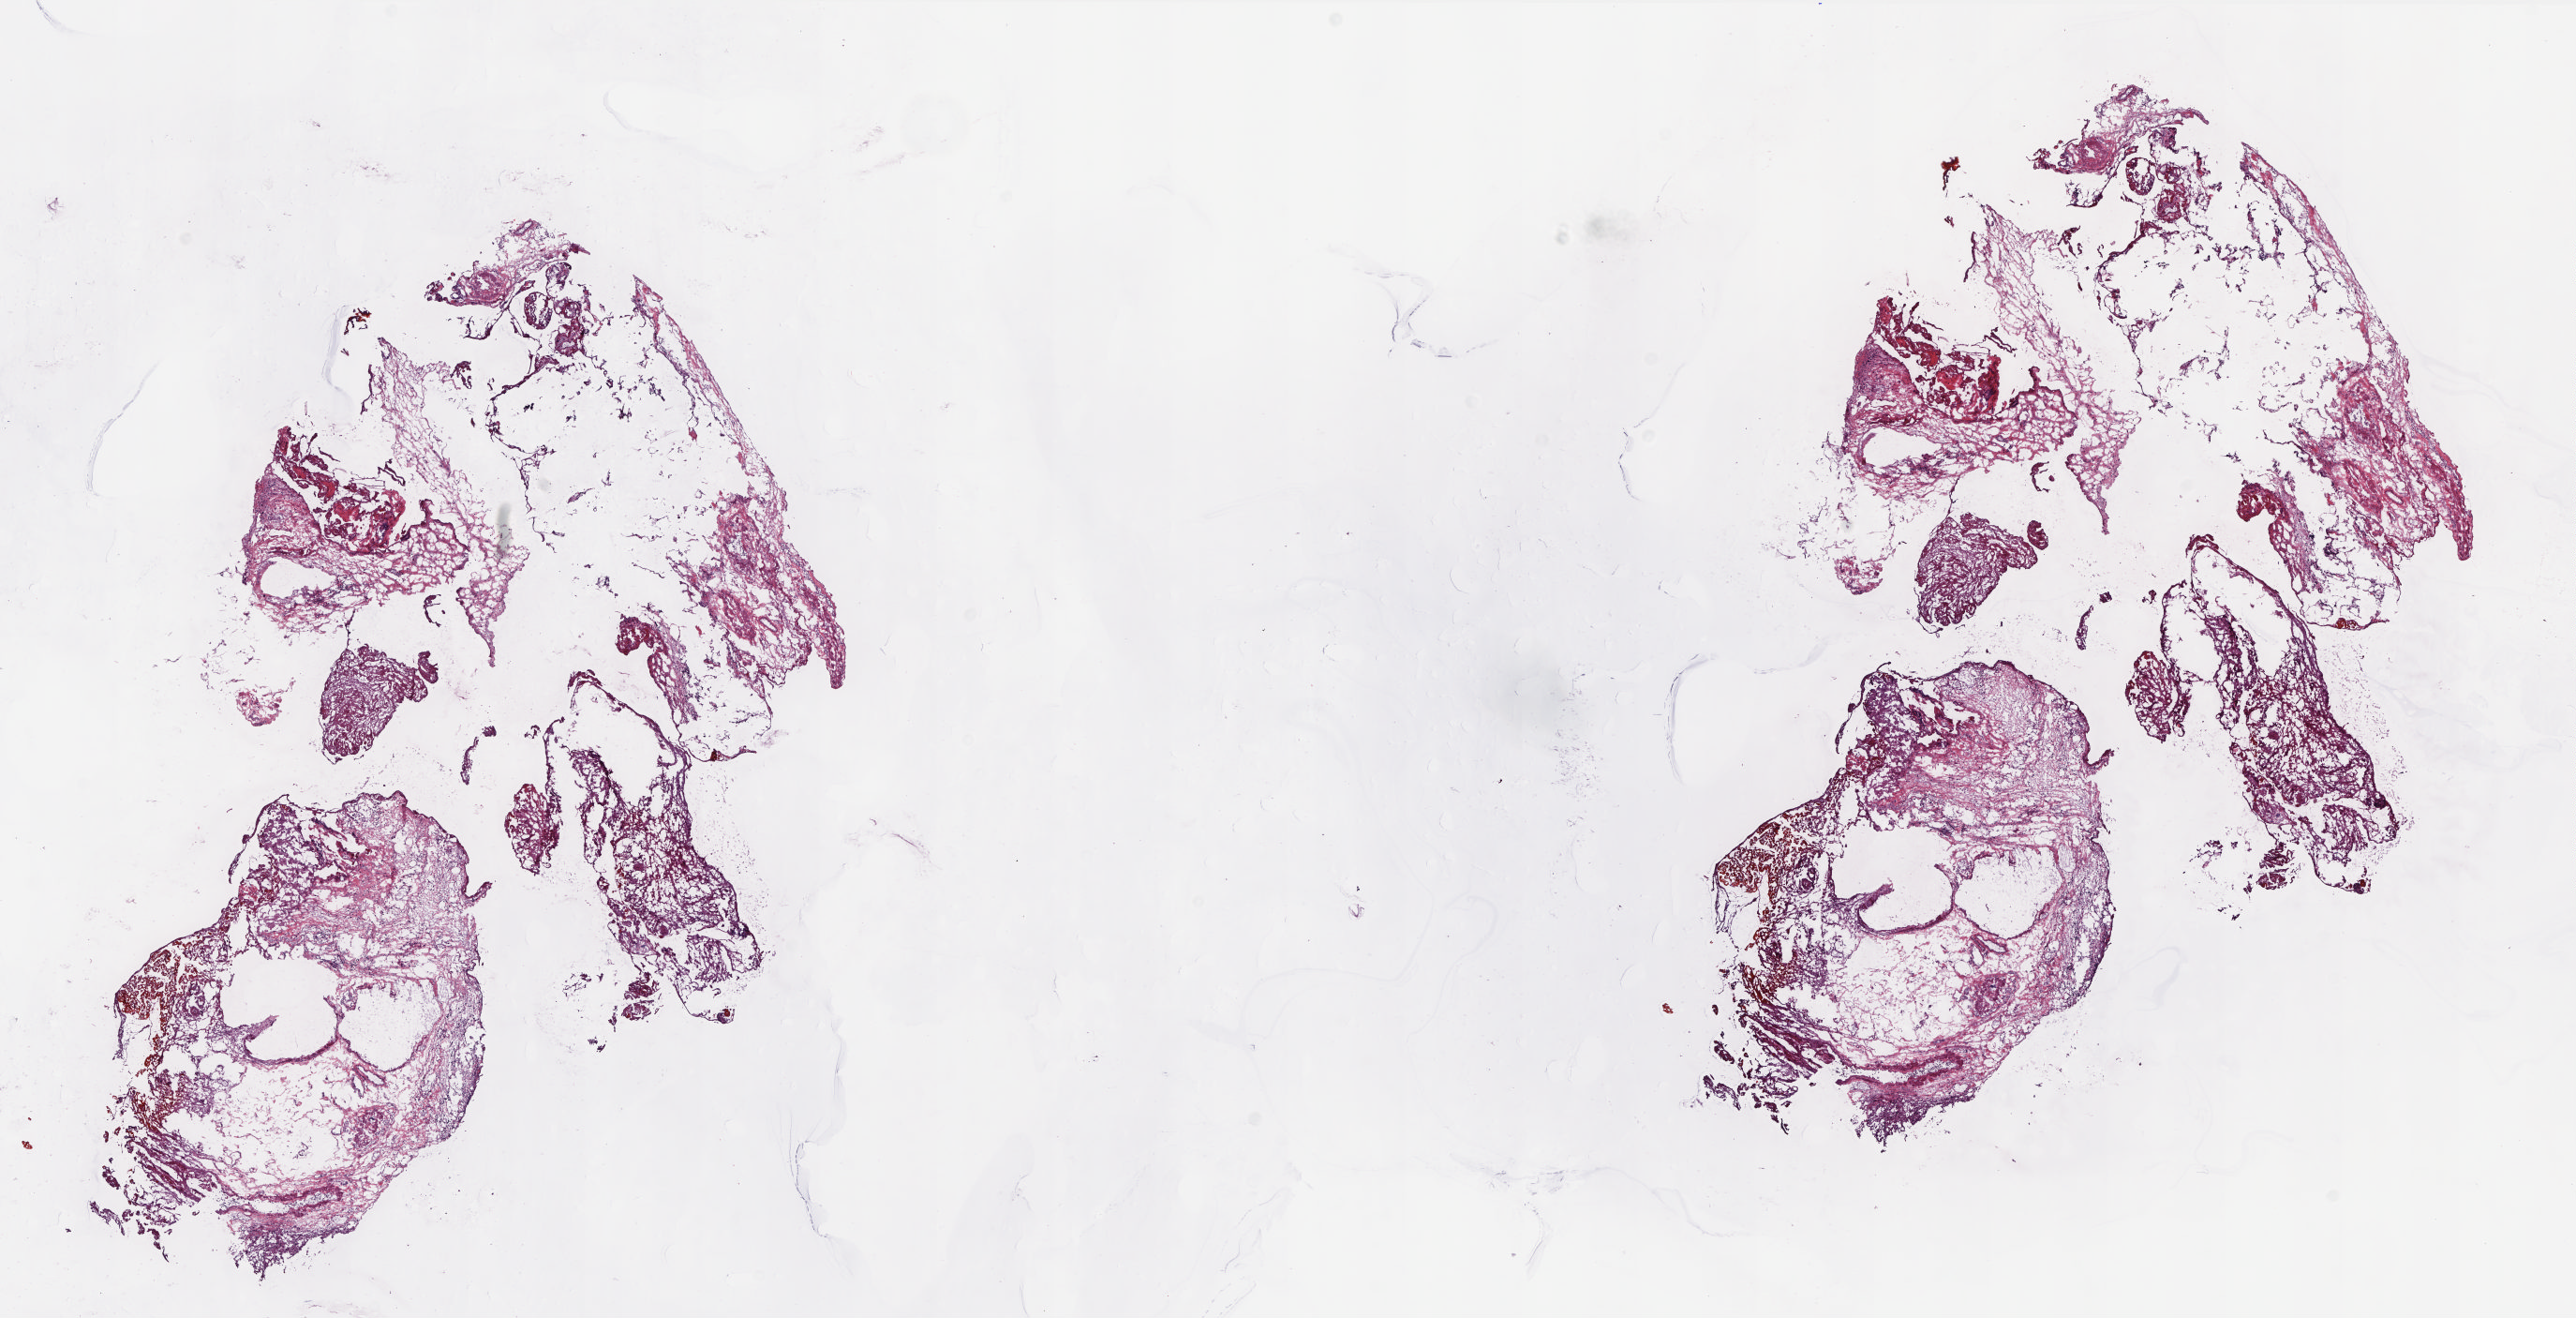
Digitized H&E-stained tissue section (whole slide) — a low-resolution overview of the entire scanned area, about 22.0 x 11.2 mm (slide scanned at 20x), frozen section, solid tissue normal (non-tumour tissue) sample from the retroperitoneum and peritoneum. Female patient; age at initial diagnosis 70 years. Pathologist review of this section (percent, as recorded): tumour cells 0%, tumour nuclei 0%, normal cells 100%, stromal cells 0%, necrosis 0%. Infiltration values recorded for this section: lymphocyte infiltration 2%, monocyte infiltration 1%, neutrophil infiltration 0%.
- this section: solid tissue normal sample (biorepository sample class)
- patient diagnosis: Dedifferentiated liposarcoma (retroperitoneum)